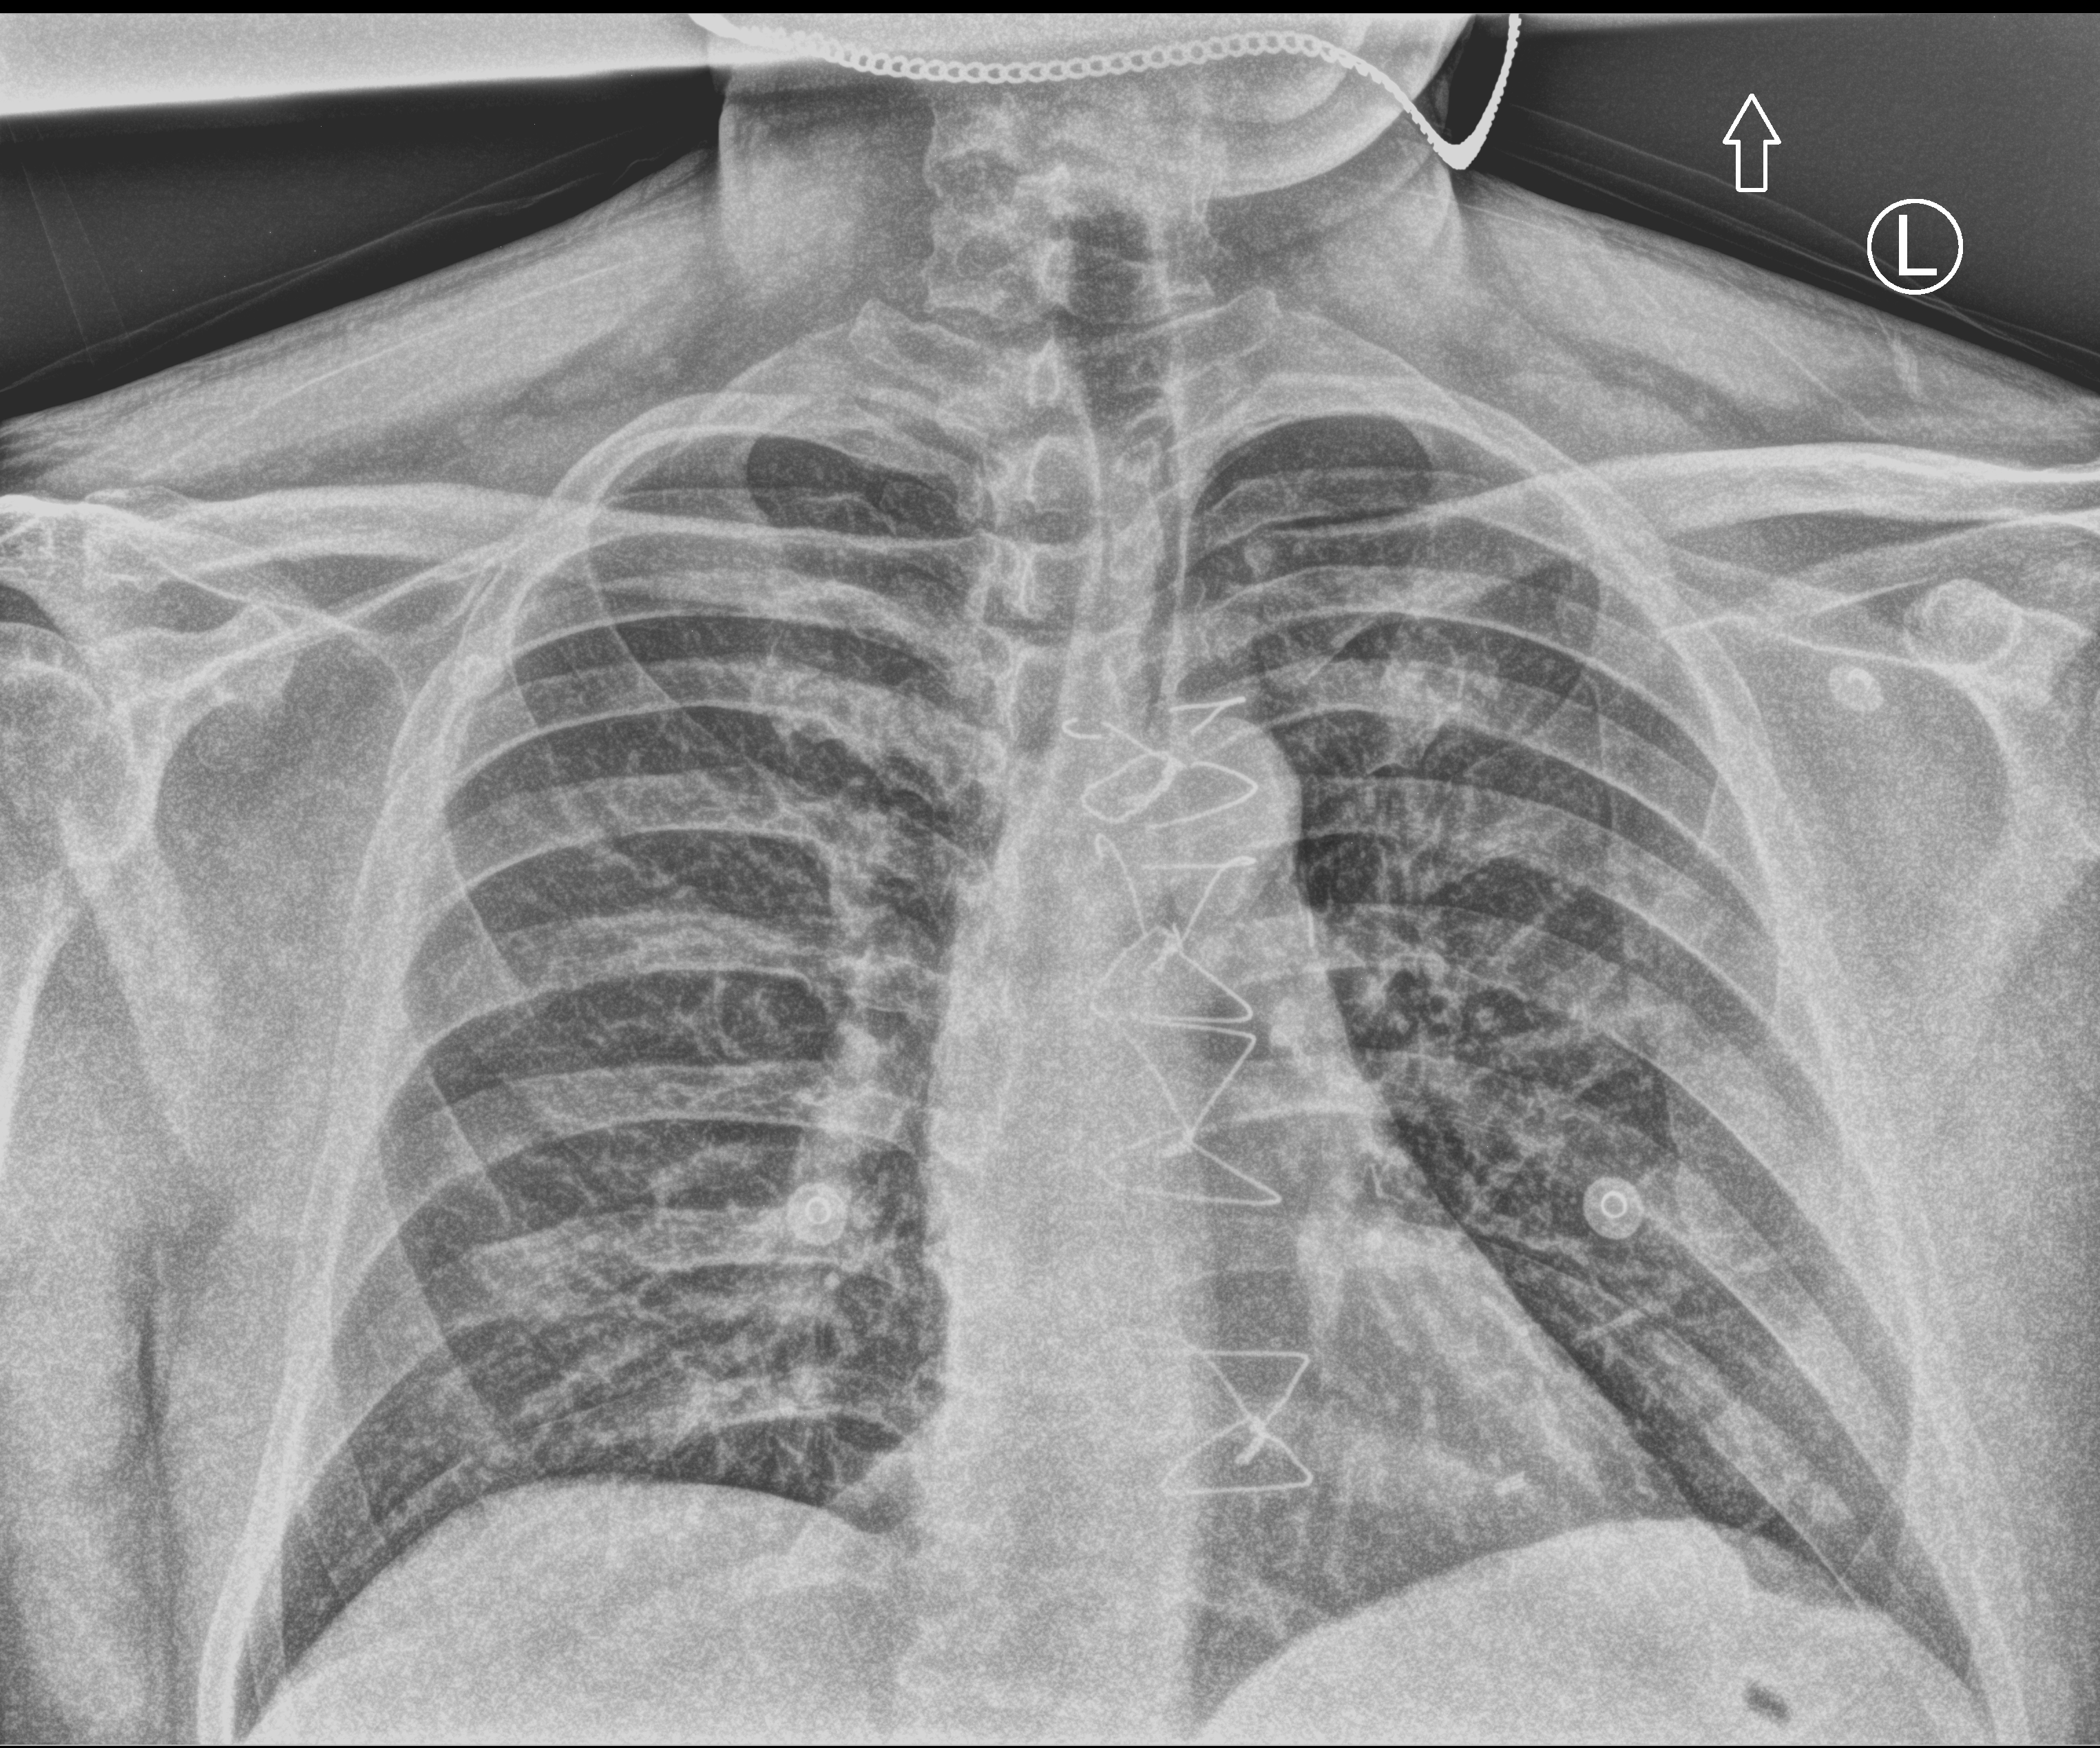
Chest X-ray (portable), anteroposterior (AP) projection. Patient hospitalised with COVID-19; male, aged 18–59 years.
Hospital-stay facts (about this admission, not read from this image; timing relative to this image not recorded): admitted to intensive care during this hospital stay: no; length of hospital stay: 2 days; hypertension (admission record): yes.